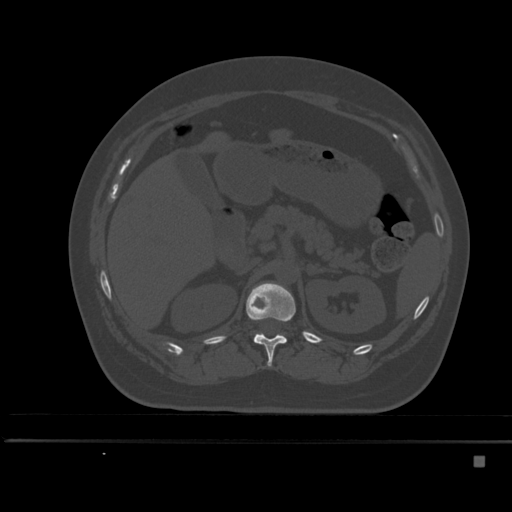
CT including the spine, one axial slice; position 209 of 495 along the scan axis; bone window (W 1800 / L 400 HU); 1.5 mm slice thickness; 512 × 512 image matrix, field of view 404 × 404 mm. Patient: female, 33 years. From the clinical record (not read from this slice): primary cancer: breast; vertebrae with lytic lesions (as recorded): T1.
Structures marked on this image (semi-automatically segmented with operator editing):
- L1 vertebra: box from (x=254, y=335) to (x=256, y=338) px
- T12 vertebra: (x=246, y=282)–(x=296, y=367)